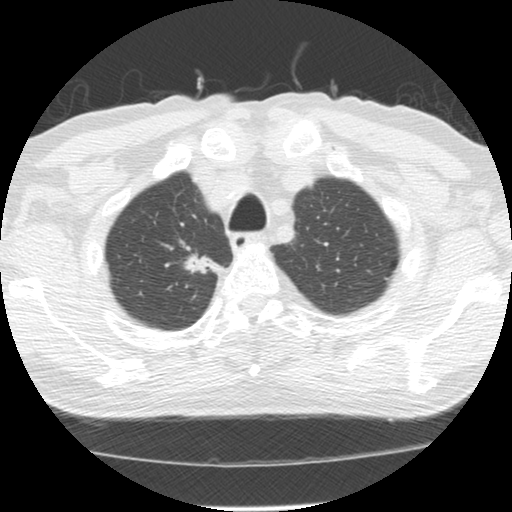
Axial slice from a low-dose chest CT screening exam. First (baseline) screen. Lung window (W 1500 / L -600 HU). Slice 26 of 139 in the series. 512 × 512 image matrix, field of view 310 × 310 mm. Male participant, aged 64 years at enrolment.
• Lesion marked by an expert reader, bounding box [x1, y1, x2, y2] px = [177, 239, 224, 280].
• Screening reader's record for this exam (one nodule recorded; not confirmed to be the boxed lesion): non-calcified nodule or mass ≥4 mm, right upper lobe, 20 × 13 mm, spiculated (stellate) margins, soft tissue attenuation.
• Participant outcome: lung cancer diagnosed 73 days after this screen — adenocarcinoma, NOS, right upper lobe, moderately differentiated (G2), stage IA (AJCC 6th edition), 17 mm at pathology.